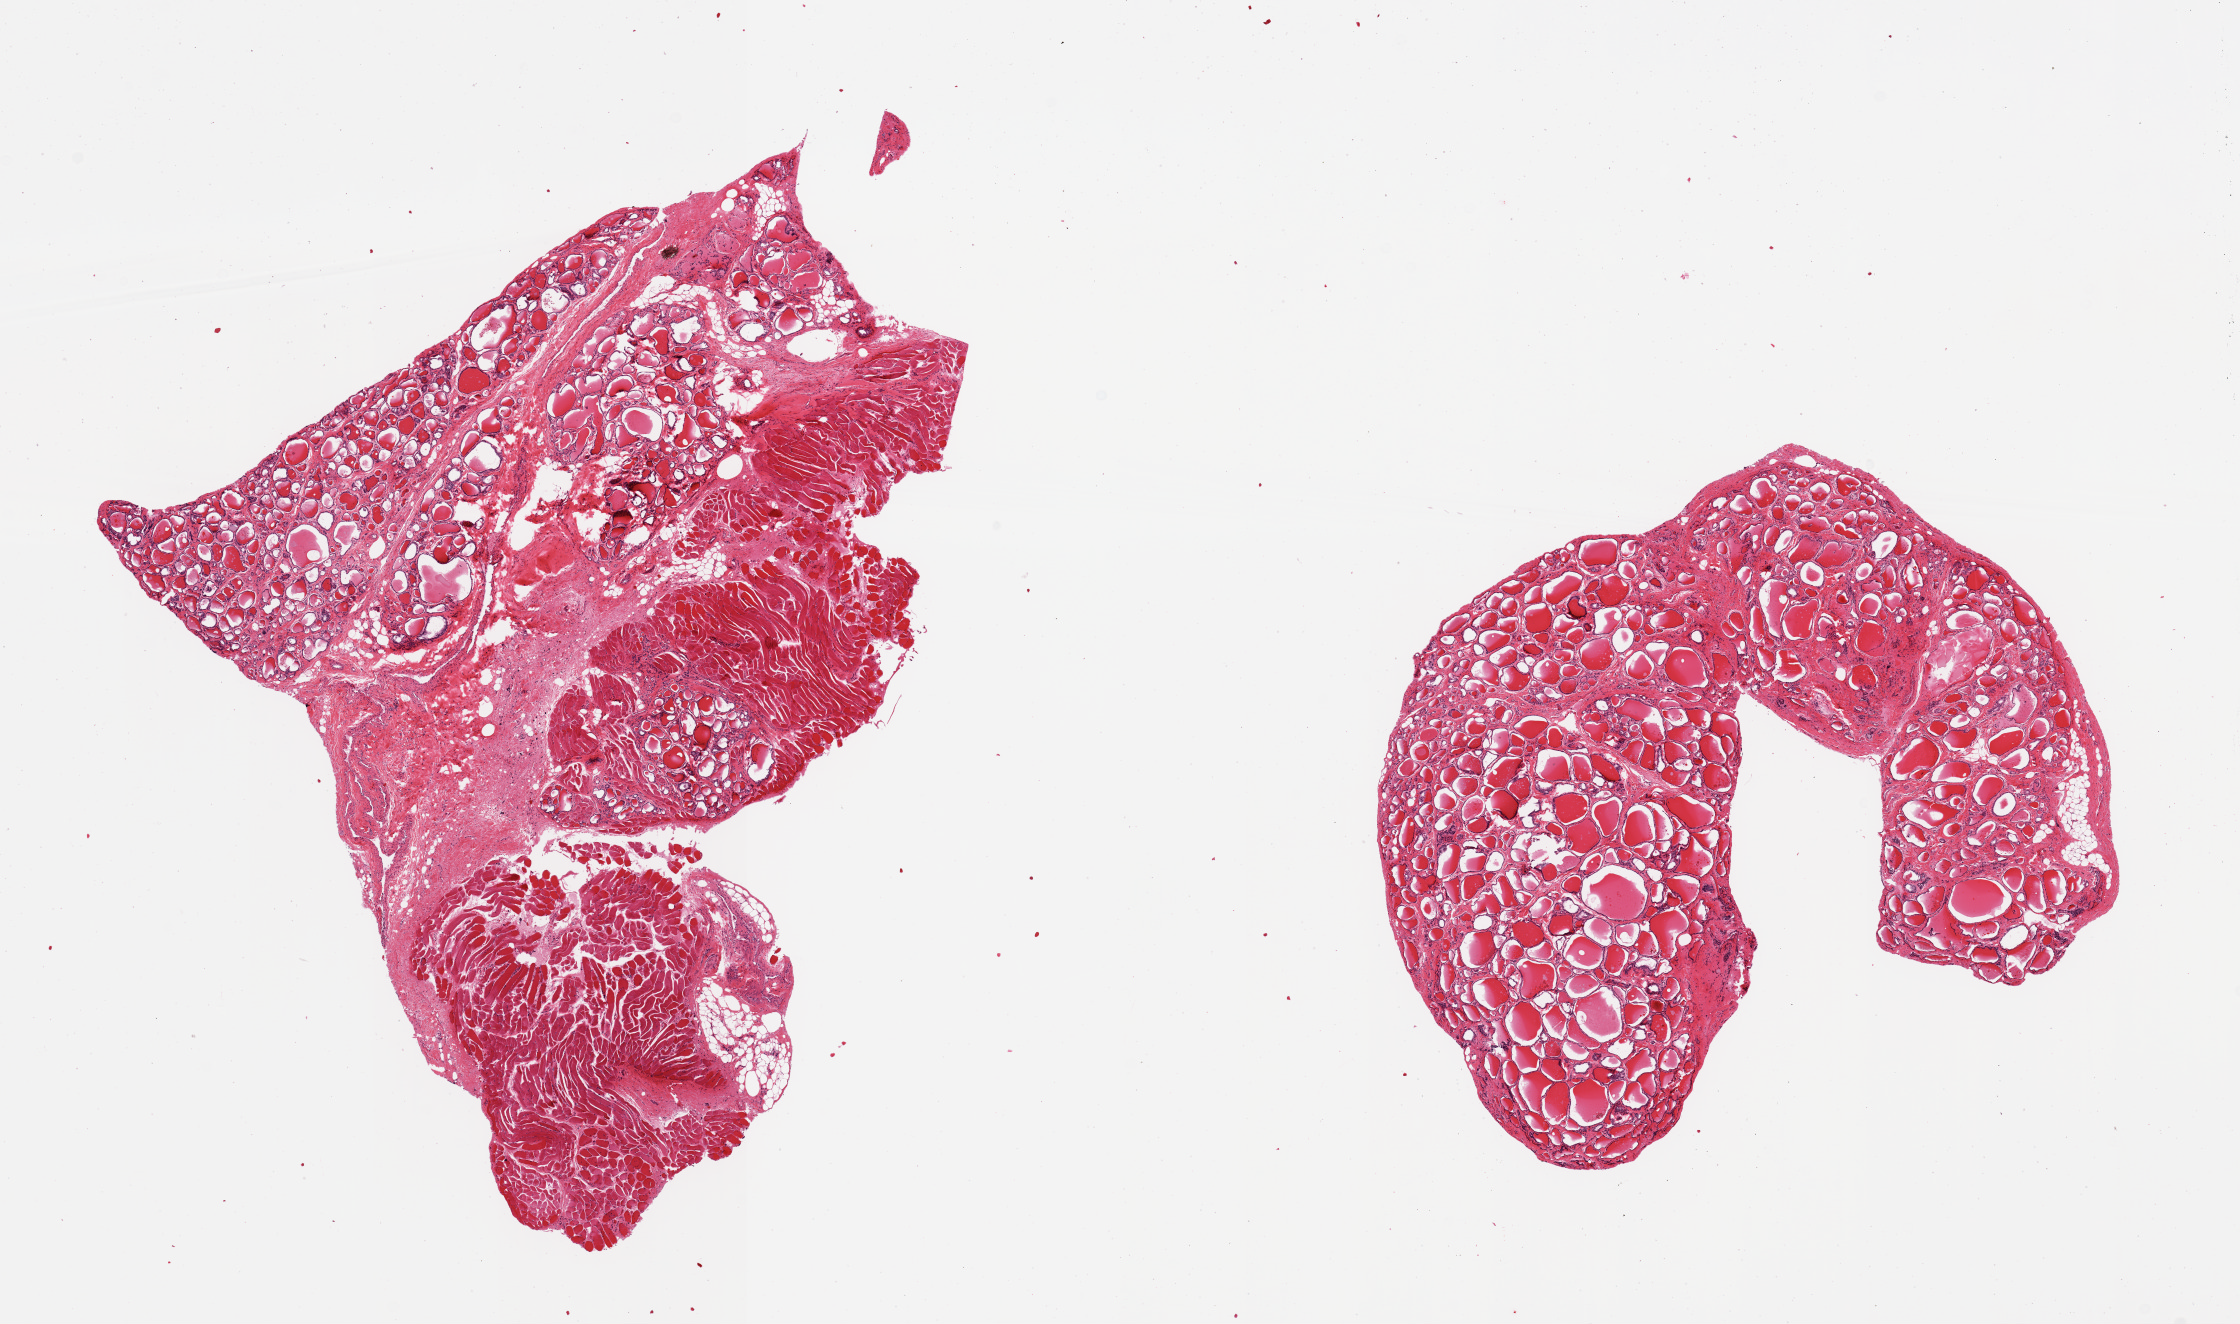
Digitized haematoxylin and eosin-stained section — whole scanned area (about 17.7 x 10.5 mm, acquisition: 20x scan) shown as a low-resolution overview. PAXgene-fixed, paraffin-embedded tissue. Sampled site (target tissue): thyroid. Donor tissue sample. Donor: female.
Reviewer comment on this tissue sample: 2 pieces, one is ~50% skeletal muscle, fat and fibrous tissue.